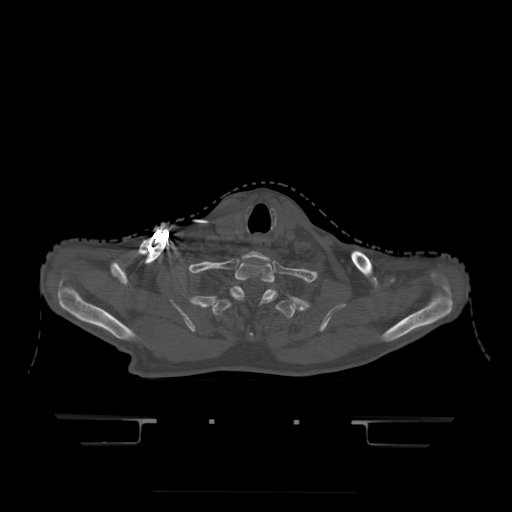
CT including the spine, one axial slice. Position 395 of 522 along the scan axis. Bone window (W 1800 / L 400 HU). 1.25 mm slice thickness. 512 × 512 image matrix. Patient age 68 years. From the clinical record (not read from this slice): primary cancer: urothelial.
Annotated regions visible in this slice (semi-automatic segmentation, software-assisted and operator-edited):
- T1 vertebra: bounding box [x1, y1, x2, y2] px = [230, 262, 278, 302]
- T2 vertebra: [213, 287, 295, 340]